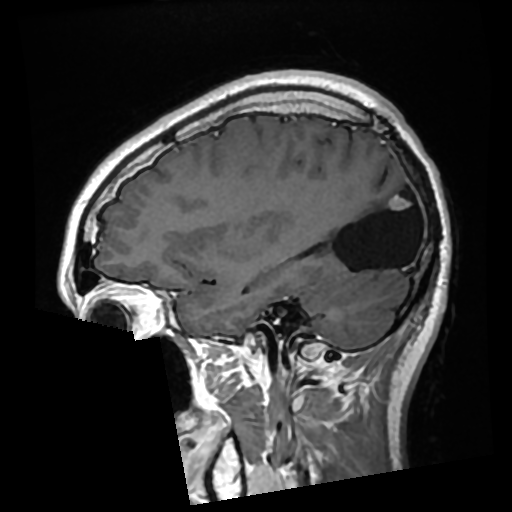
Brain MRI from a brain-tumour surgery series, one sagittal slice; slice 93 of 276 in the series (ordered by position); T1-weighted post-contrast; 0.7 mm slice thickness; 512 × 512 image matrix, field of view 250 × 250 mm. From the clinical record (not read from this slice): histopathology: Glioma with ependymal features; WHO grade: 2.
Annotated regions visible in this slice (outlined manually by an expert reader):
- previous resection cavity: box from (x=327, y=182) to (x=415, y=270) px
- tumour: (x=389, y=196)–(x=411, y=211)